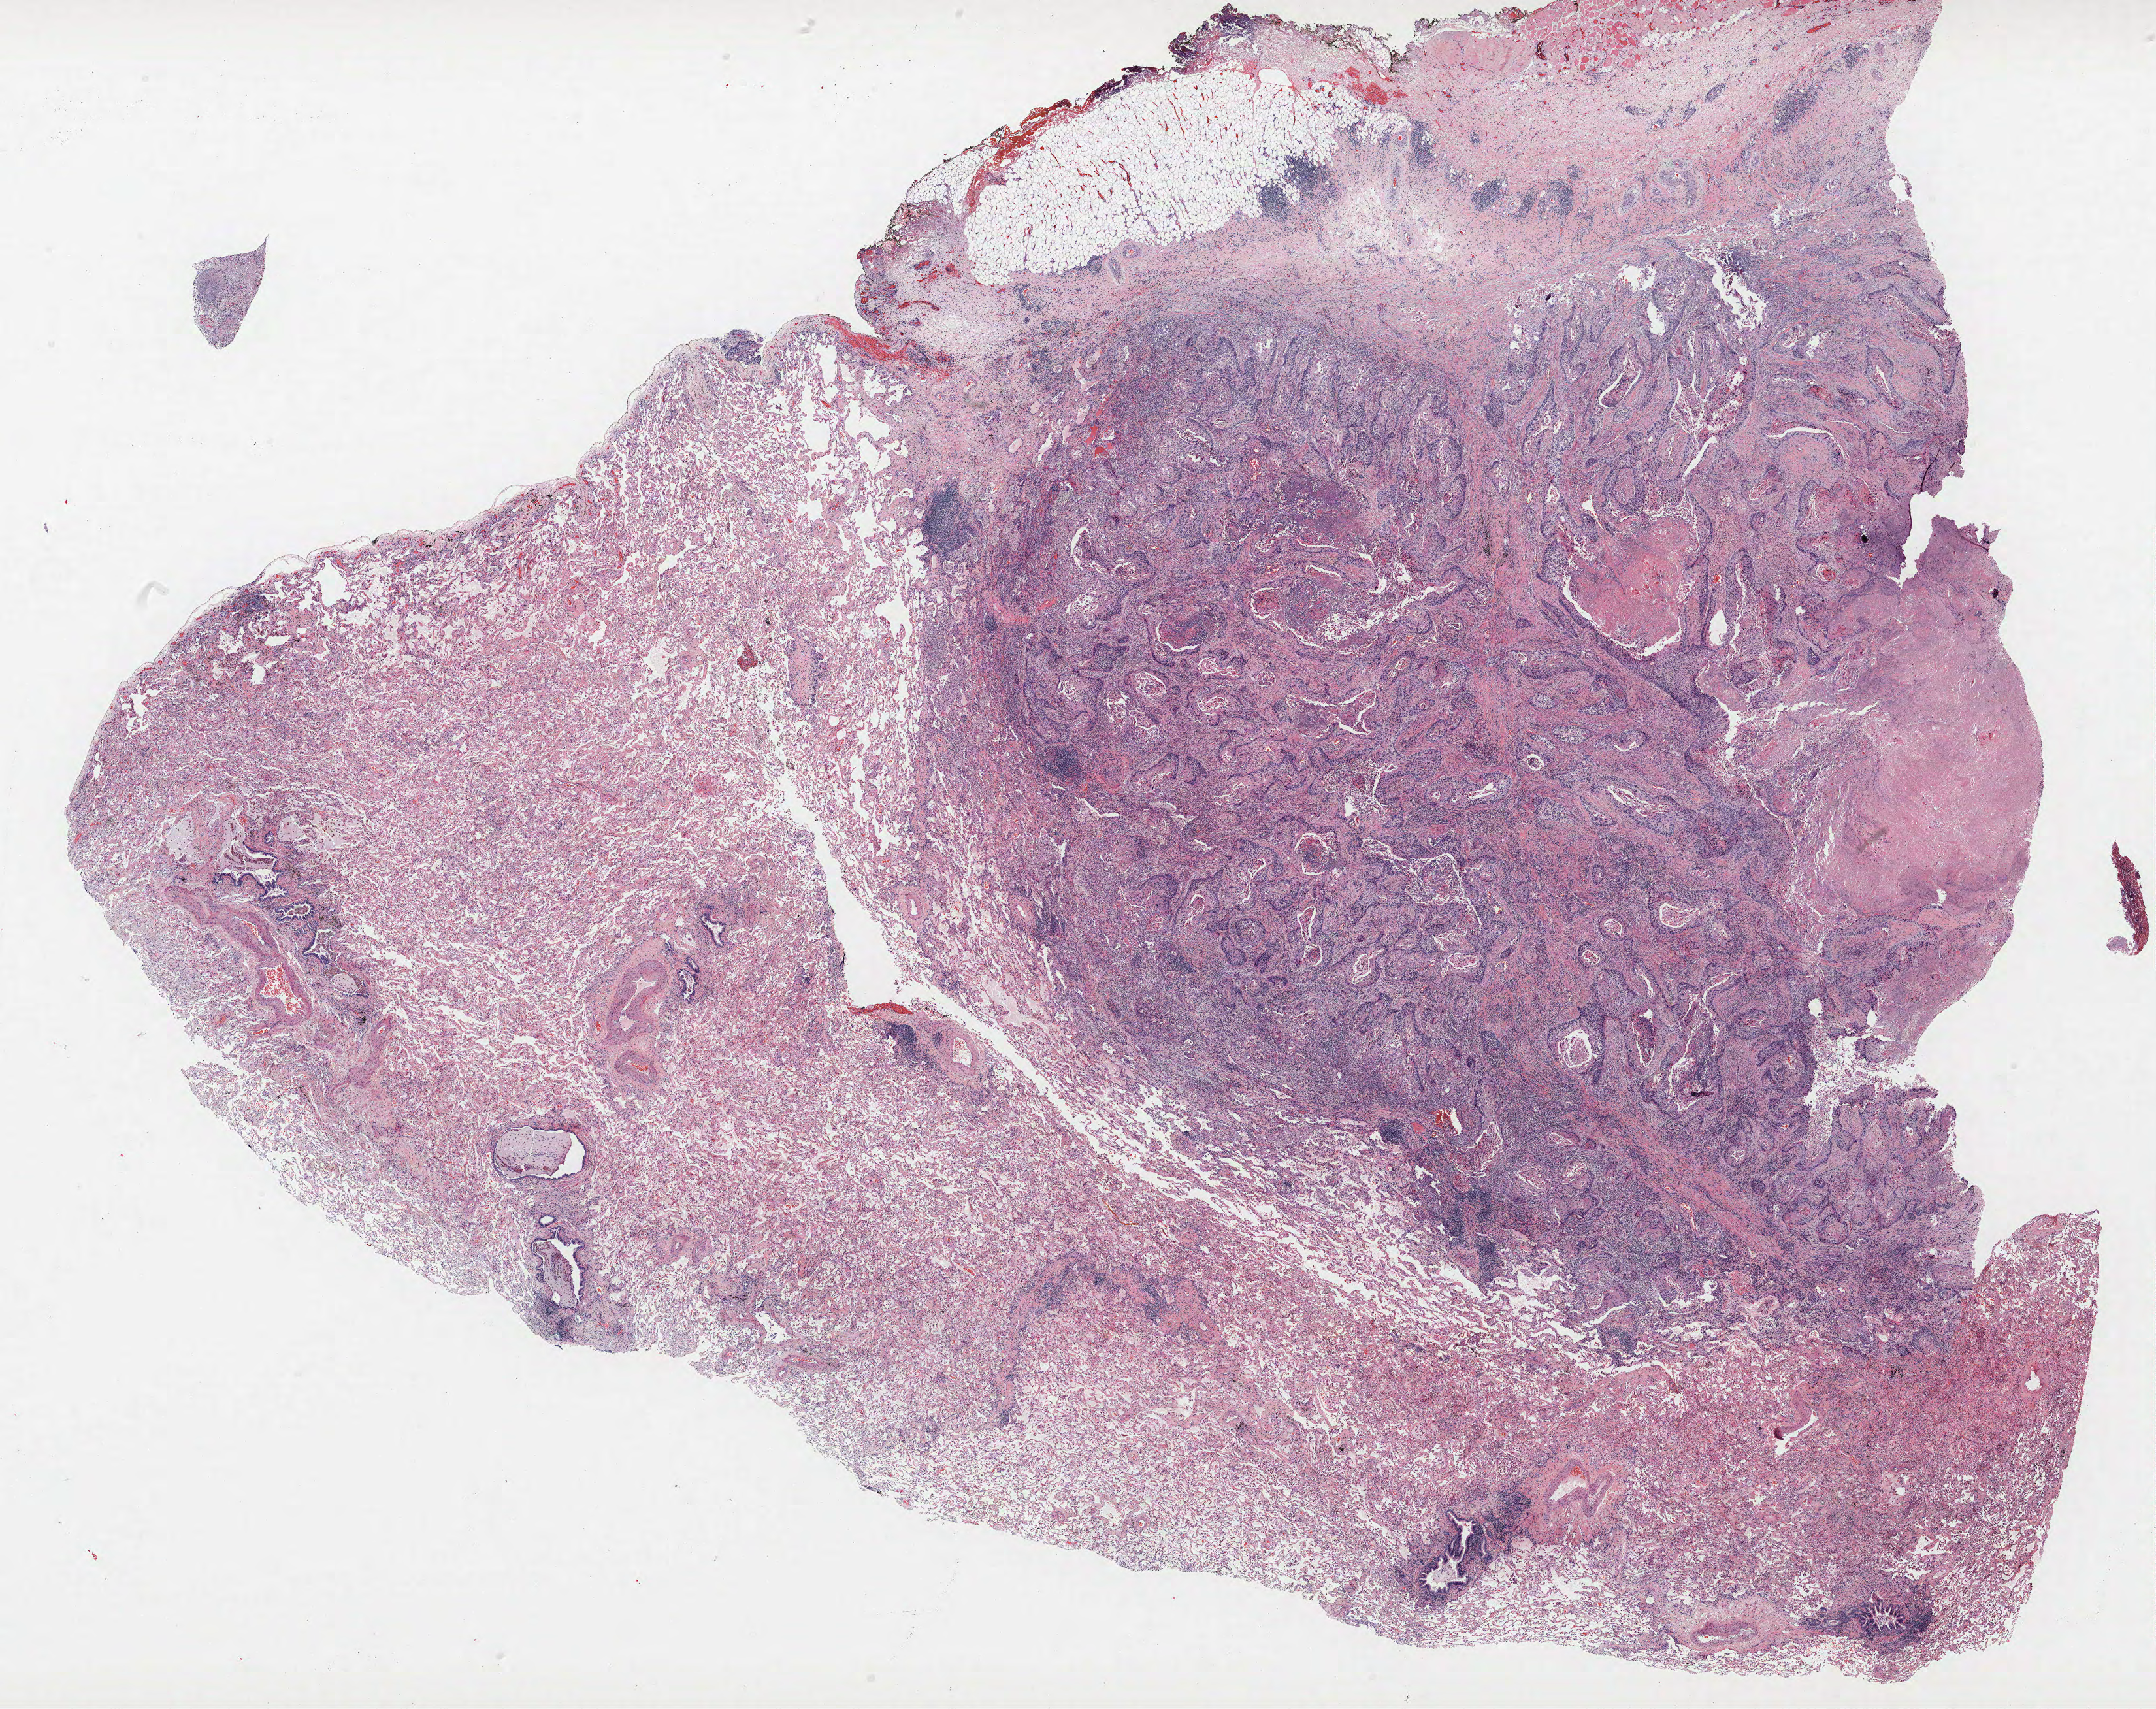
H&E-stained whole-slide image, a low-resolution overview of the entire scanned area, about 26.4 x 20.9 mm (from a 40x scan). FFPE section. Lung. Female, age 59 at enrolment. Current smoker at enrolment. Grade: moderately differentiated (G2).
Tumour size (pathology): 28 mm. ICD-O-3 topography: upper lobe of lung (C34.1). Stage (AJCC 6th edition): IB. Participant's lung-cancer diagnosis: Squamous cell carcinoma, NOS. Primary tumour location (clinical record): right upper lobe.